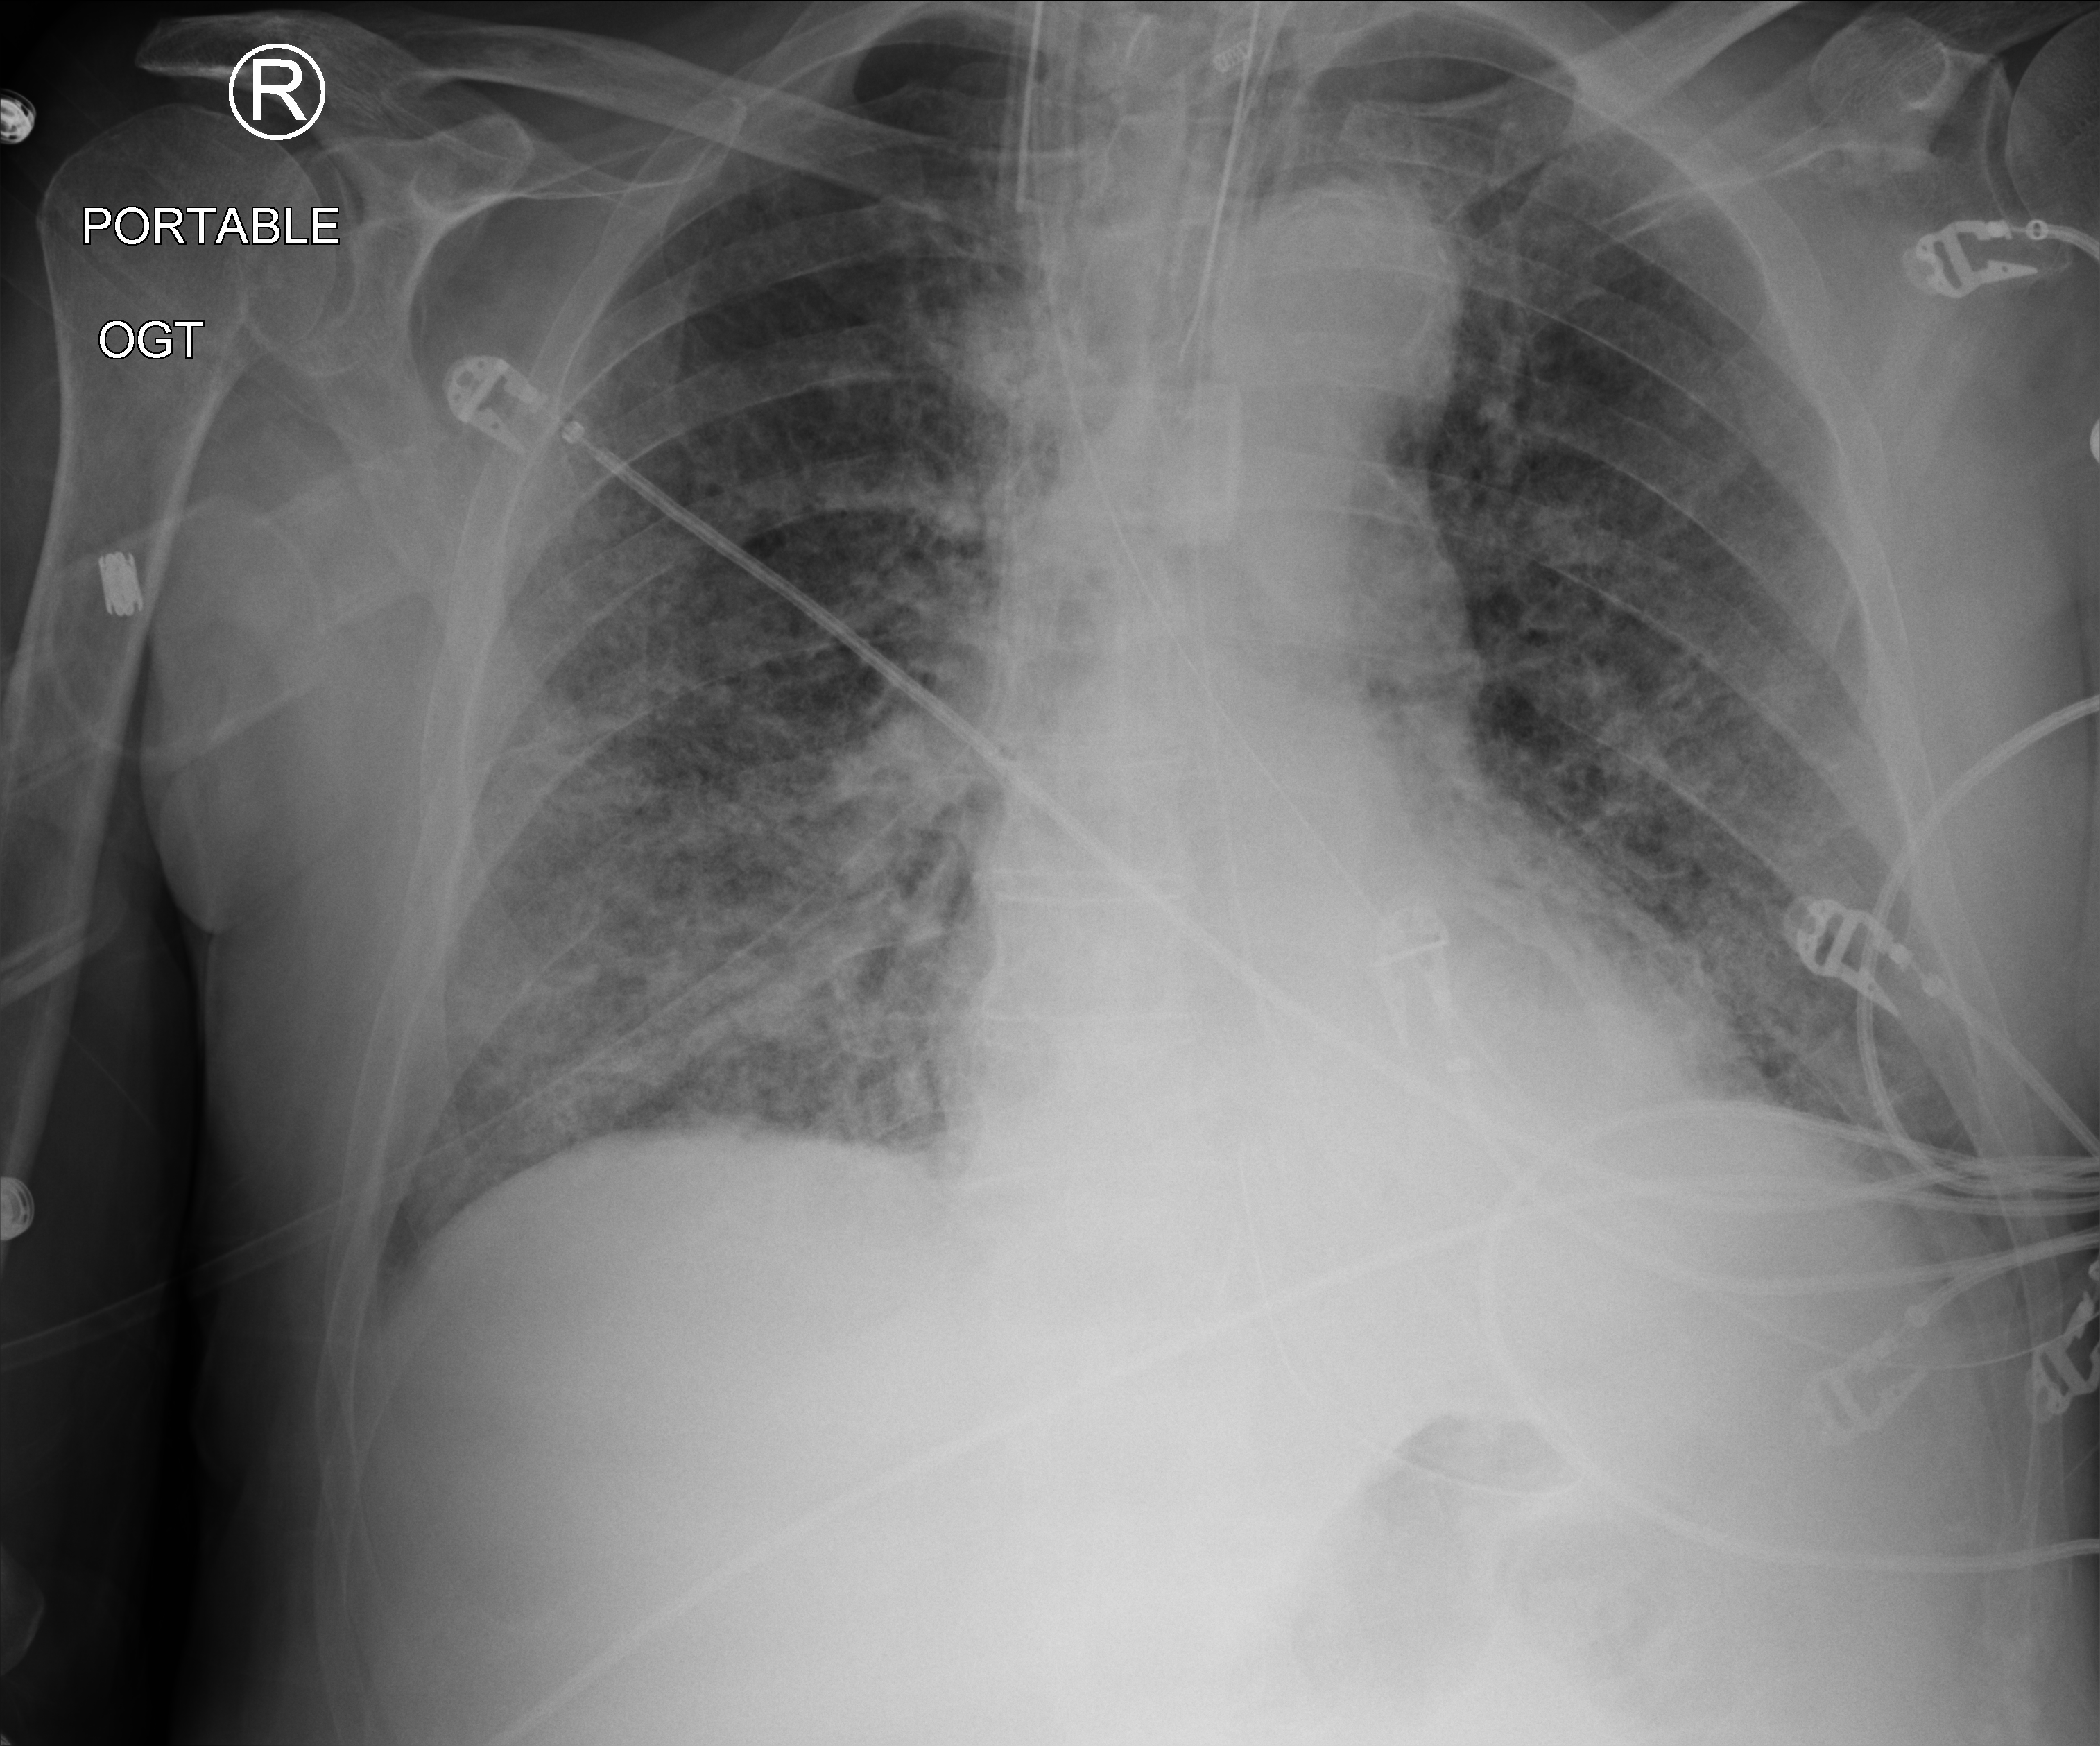
Portable chest radiograph; anteroposterior (AP) projection. Male patient hospitalised with COVID-19, age 75–90 years.
Hospital-stay facts (about this admission, not read from this image; timing relative to this image not recorded): COPD (admission record): no; admitted to intensive care during this hospital stay: yes; smoking status (admission record): former.